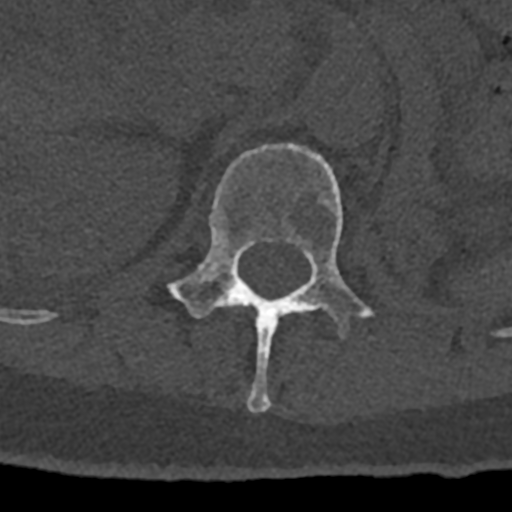
CT including the spine, one axial slice. Position 441 of 797 along the scan axis. Reconstruction kernel Br40s/3. 120 kVp. Bone window (W 1800 / L 400 HU). 512 × 512 image matrix, field of view 160 × 160 mm. Patient: male, 74 years. From the clinical record (not read from this slice): primary cancer: renal; vertebrae with lytic lesions (as recorded): T10, L1, L2, L3, L4, L5.
Structures marked on this image (semi-automatically segmented with operator editing):
- L1 vertebra: bounding box [x1, y1, x2, y2] px = [167, 143, 374, 413]
- T12 vertebra: [226, 303, 241, 307]